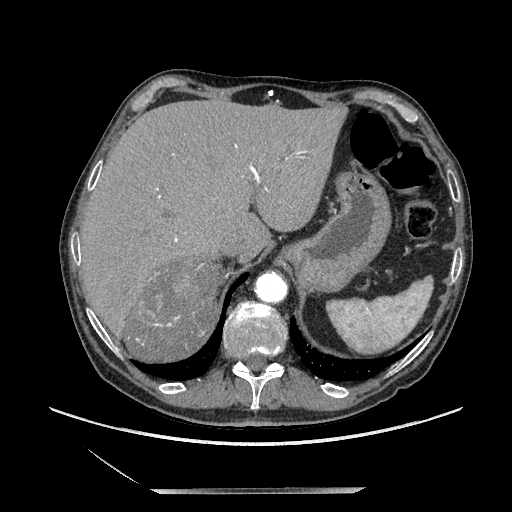
Contrast-enhanced abdominal CT, one axial slice. Position 167 of 243 along the scan axis. Soft-tissue window (W 400 / L 40 HU). 1.25 mm slice thickness. 512 × 512 image matrix, field of view 420 × 420 mm. Male patient. Case-level facts recorded for this patient, not image findings: diagnosis: adrenocortical carcinoma; tumour side: right adrenal; tumour size at pathology: 16 cm; Ki-67 index: 17 %; stage (as recorded): 3.
Structures marked on this image (semi-automatically segmented with operator editing):
- mass: bounding box (x1, y1, x2, y2) in pixels: (127, 264, 224, 361)